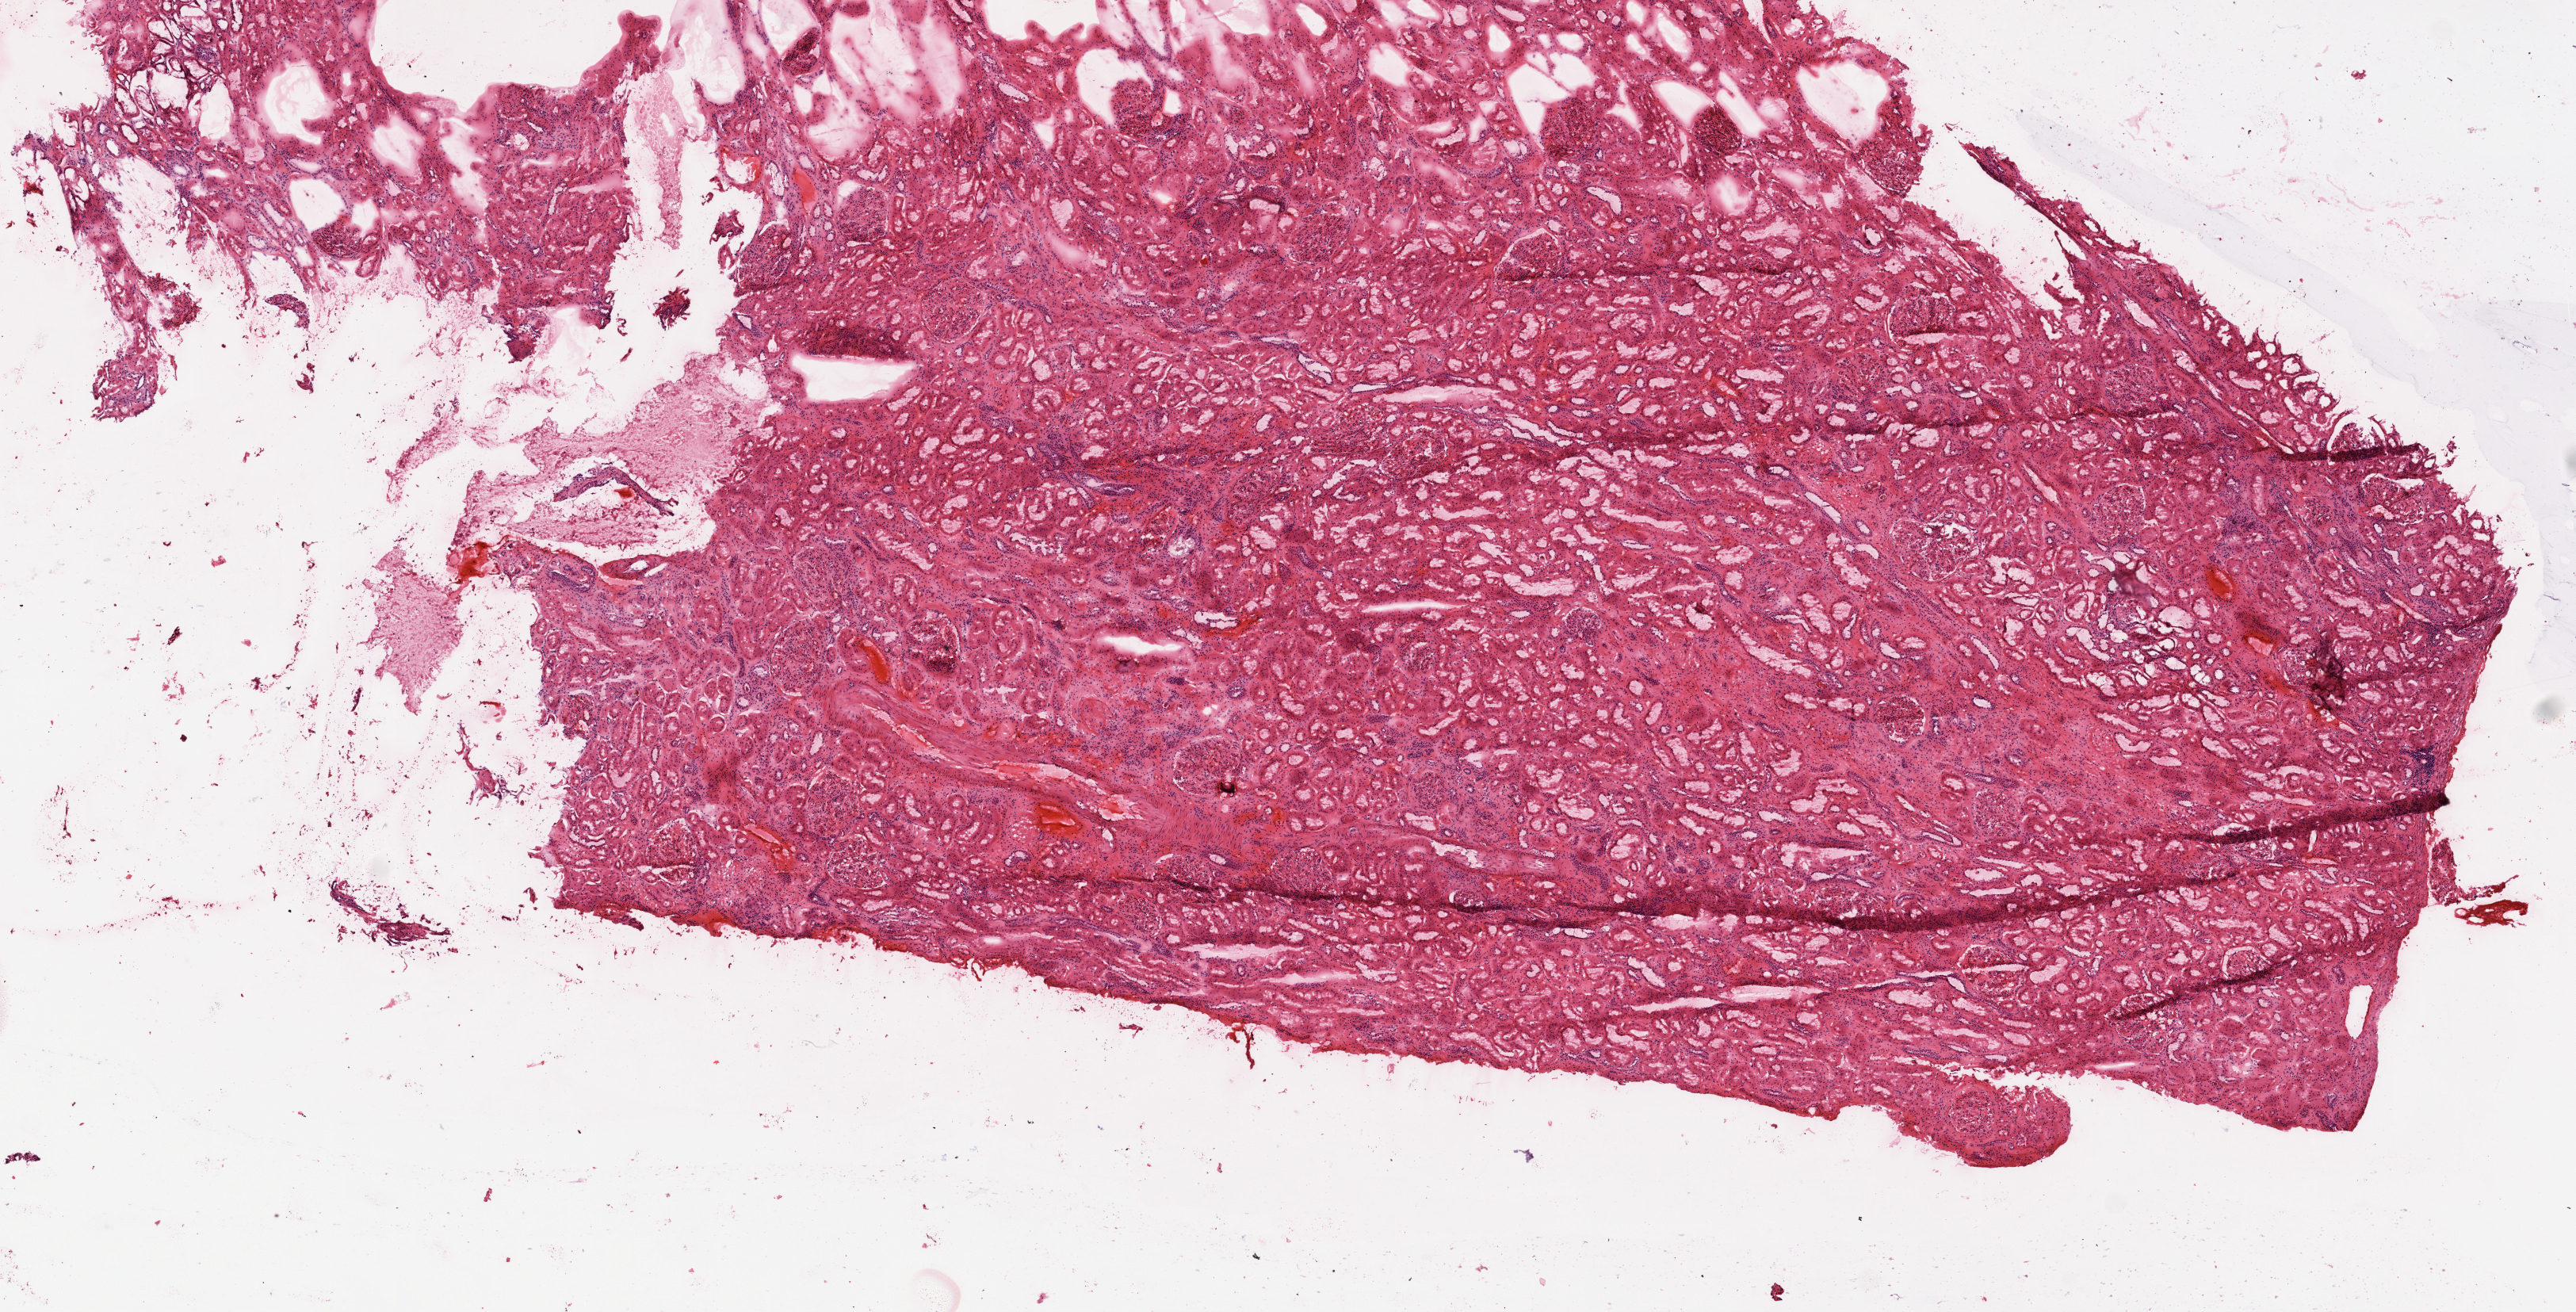
H&E whole-slide image — whole scanned area (about 13.0 x 6.6 mm, from a 20x scan) shown as a low-resolution overview, frozen section from the top of the tissue portion, sample: solid tissue normal (non-tumour tissue), kidney. Male patient; age at initial diagnosis 57 years.
This section: solid tissue normal (non-tumour) sample from the same patient. Patient diagnosis: Clear cell adenocarcinoma, NOS.